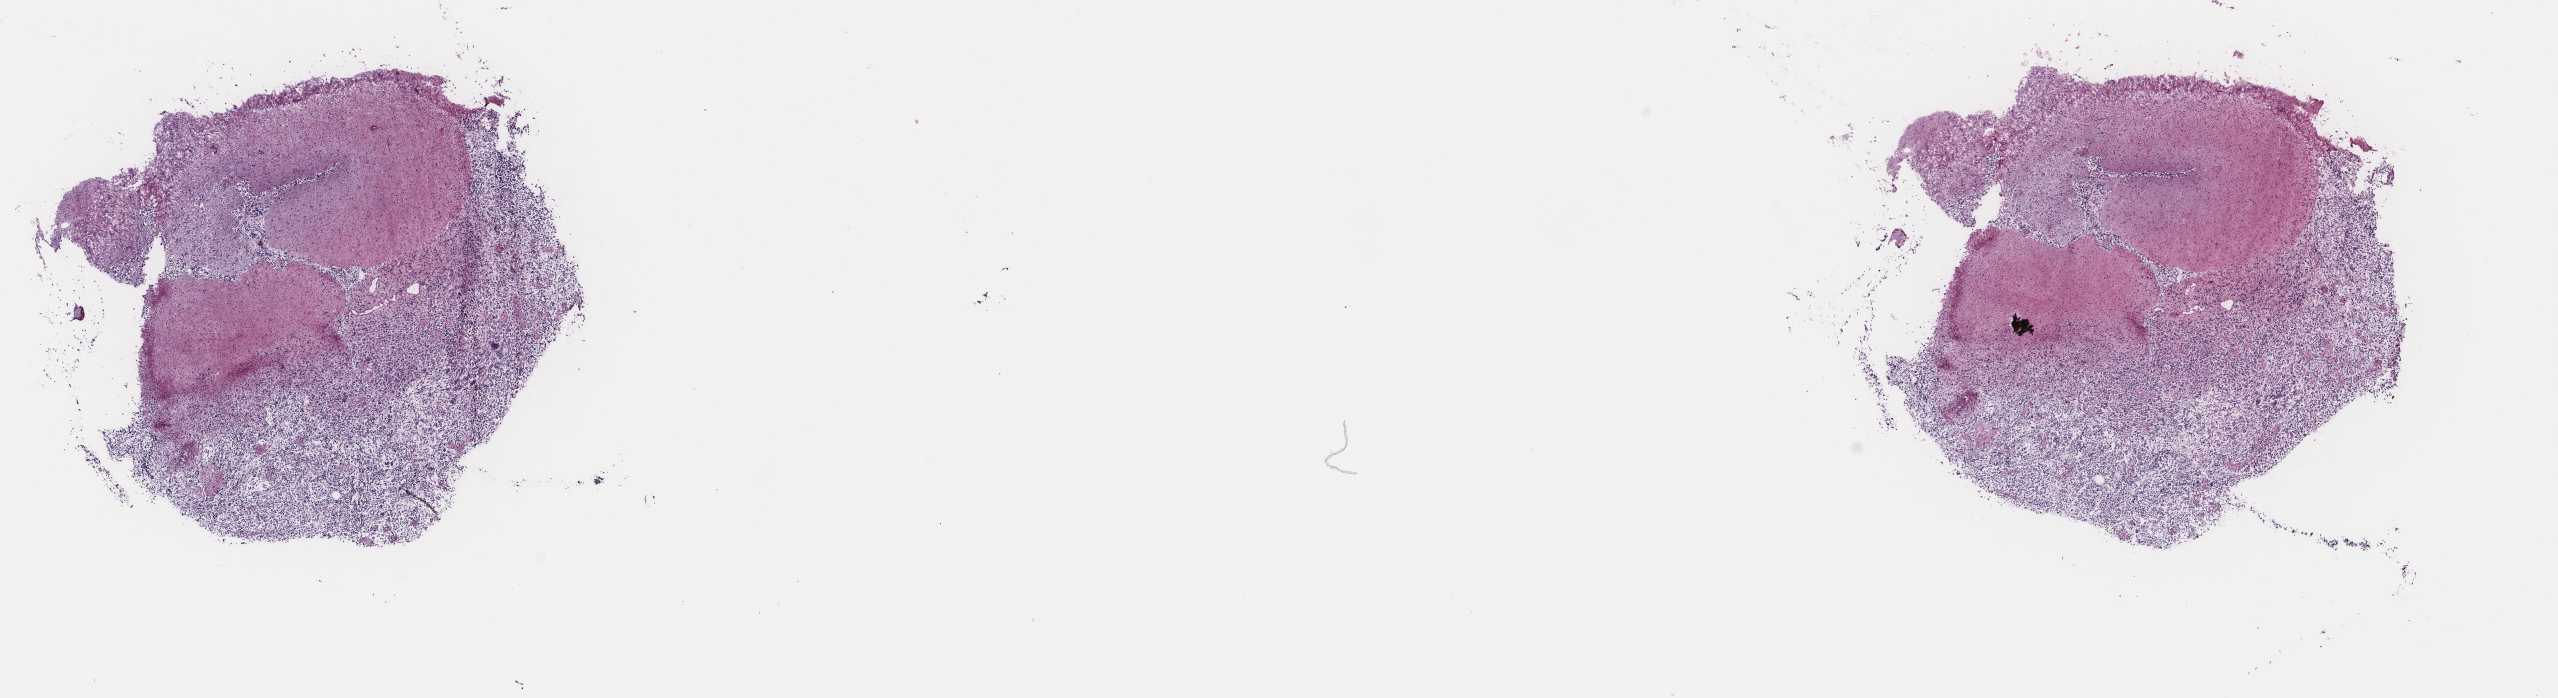
Digitized H&E-stained tissue section (whole slide) — shown as a low-resolution overview of the whole scanned area (about 20.3 x 5.5 mm, from a 40x scan); frozen section from the top of the tissue portion; brain, primary tumour sample. Female patient; age at initial diagnosis 30 years. Histologic grade: G3 (poorly differentiated). Pathologist review of this section (percent, as recorded): tumour cells 80%, tumour nuclei 90%, normal cells 5%, stromal cells 15%, necrosis 0%. Inflammatory infiltration, as recorded: lymphocyte infiltration 0%, monocyte infiltration 0%, neutrophil infiltration 0%.
• pathologic diagnosis: Oligodendroglioma, anaplastic (cerebrum)
• laterality: right